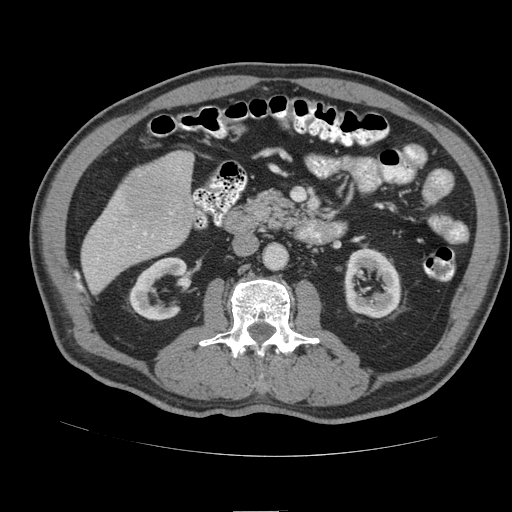
Contrast-enhanced abdominal CT (liver protocol), one axial slice; slice 29 of 105 in the series (ordered by position); reconstruction kernel STANDARD; soft-tissue window (W 400 / L 40 HU); 512 × 512 image matrix, field of view 380 × 380 mm. From the clinical record (not read from this slice): diagnosis: hepatocellular carcinoma (patient treated with transarterial chemoembolisation; whether this scan precedes or follows treatment is not stated here); TNM stage (as recorded): Stage-IIIB; Child-Pugh class: A.
Outlined on this slice (semi-automatic segmentation, software-assisted and operator-edited):
- liver parenchyma outside the tumour (the mass and vessels are separate outlines, so this box may not span the whole liver): bounding box <82,163,158,292> (left, top, right, bottom; pixels)
- mass: <126,166,173,224>